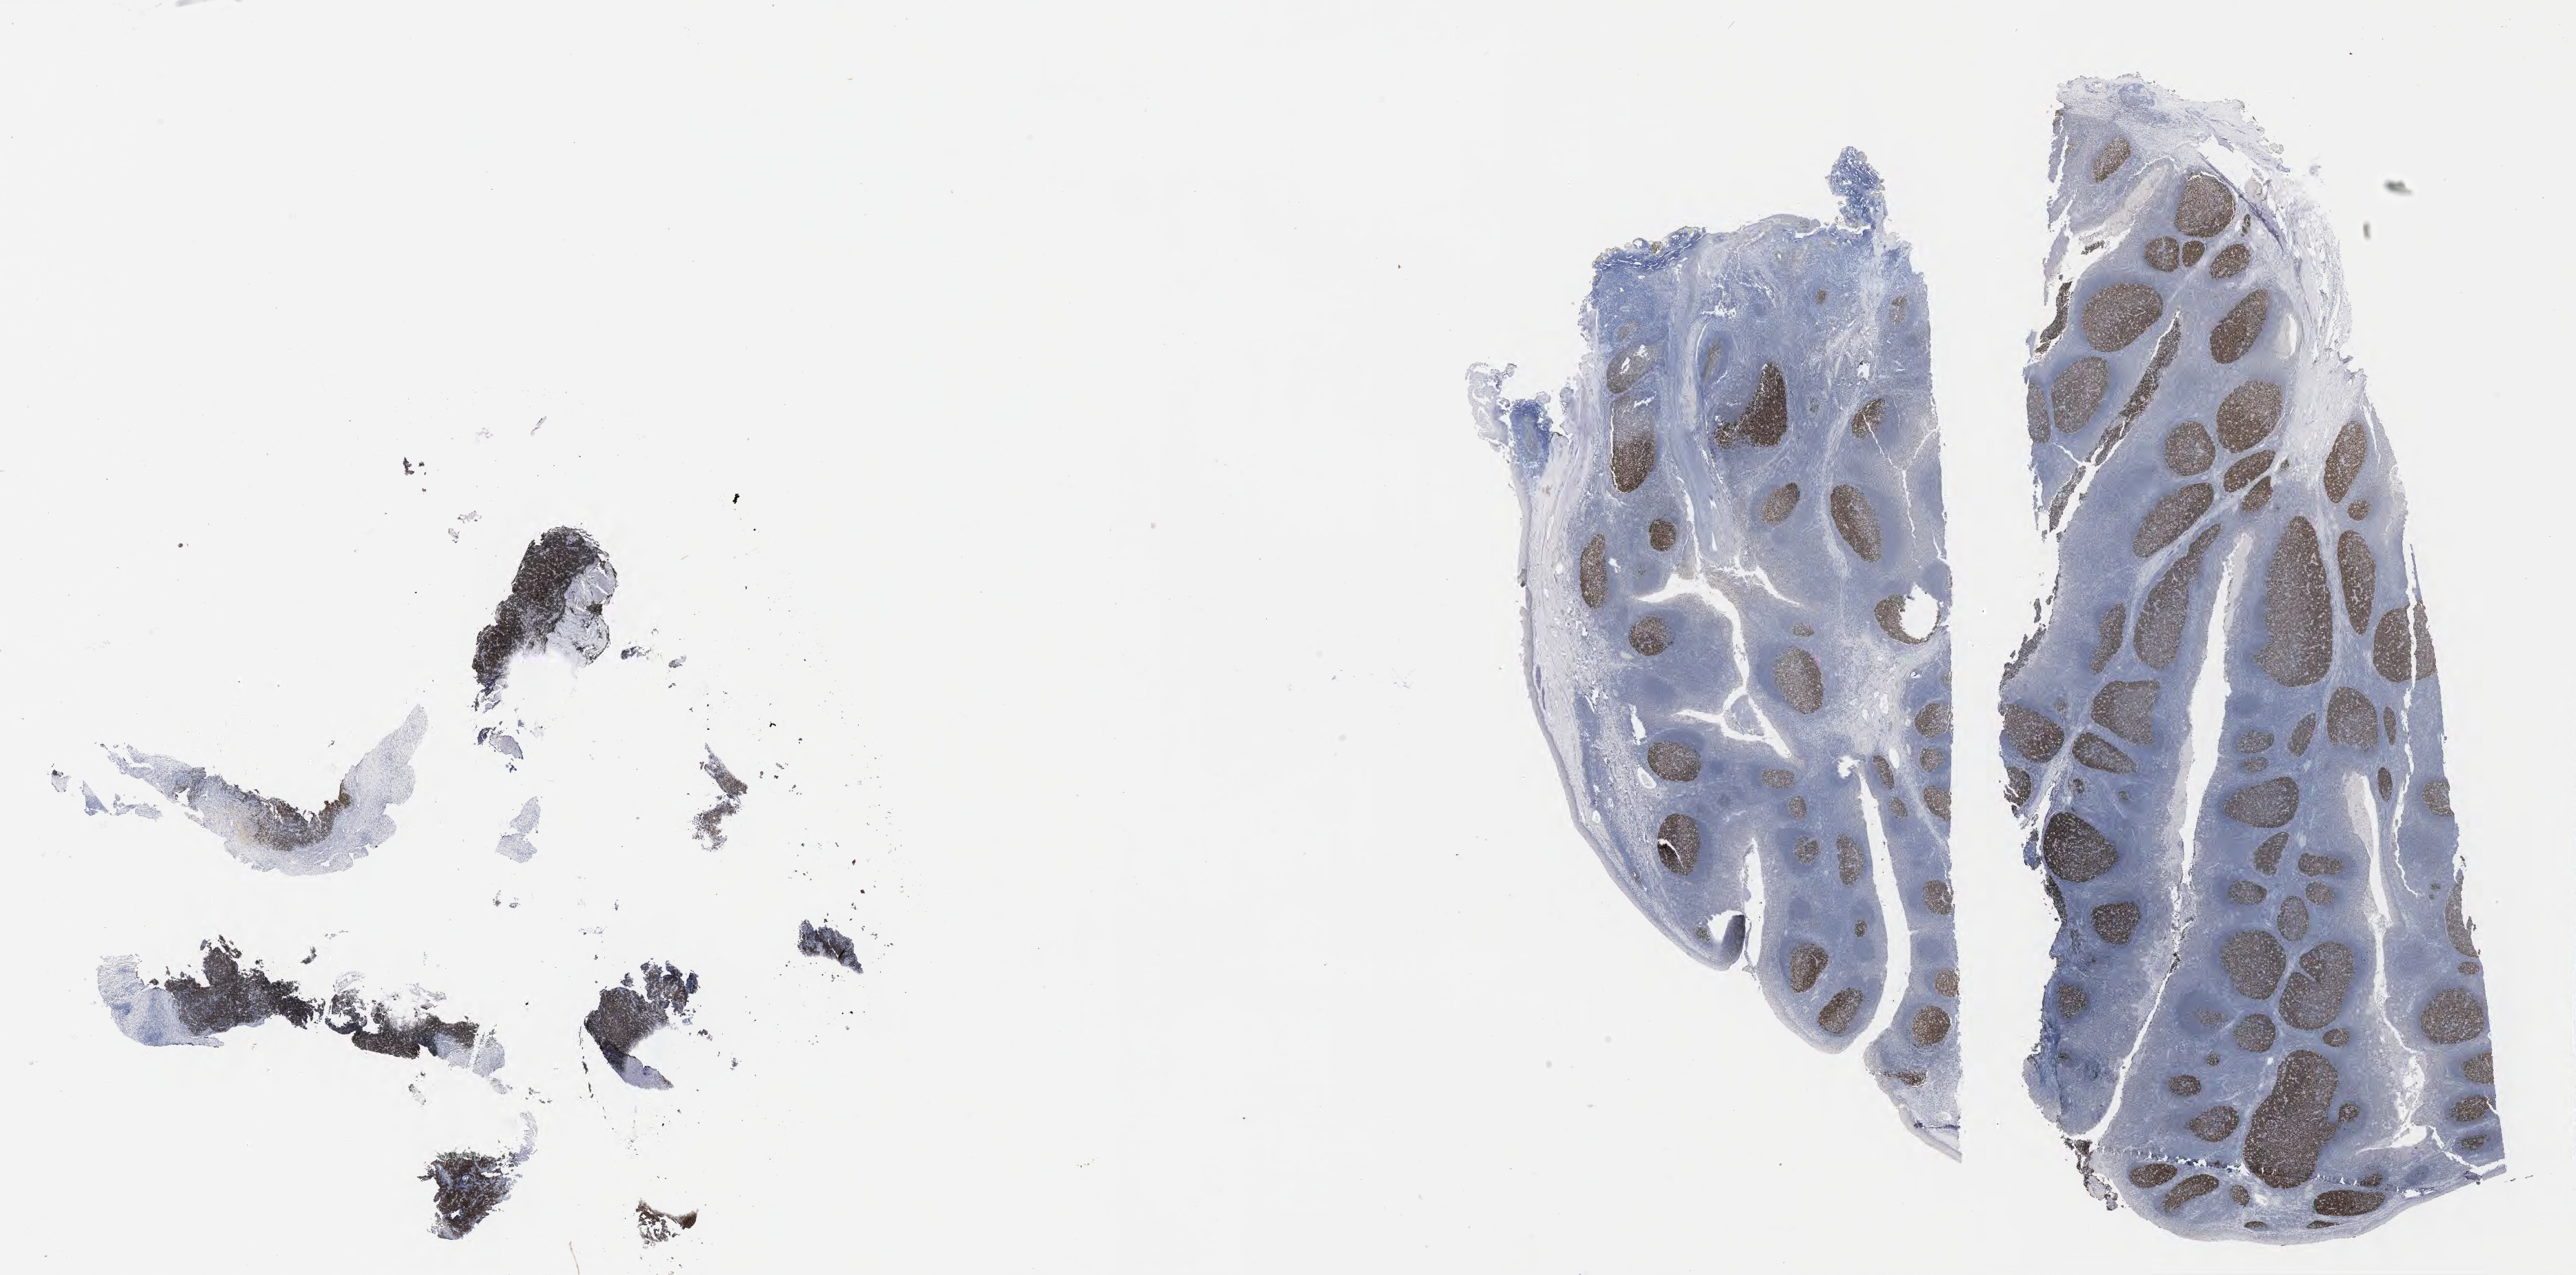
IHC for BCL6, whole-slide image, a low-resolution overview of the entire scanned area, about 30.2 x 14.9 mm, specimen: tumor tissue. Patient: female, age at initial diagnosis 9 years.
• diagnosis: Burkitt lymphoma, NOS